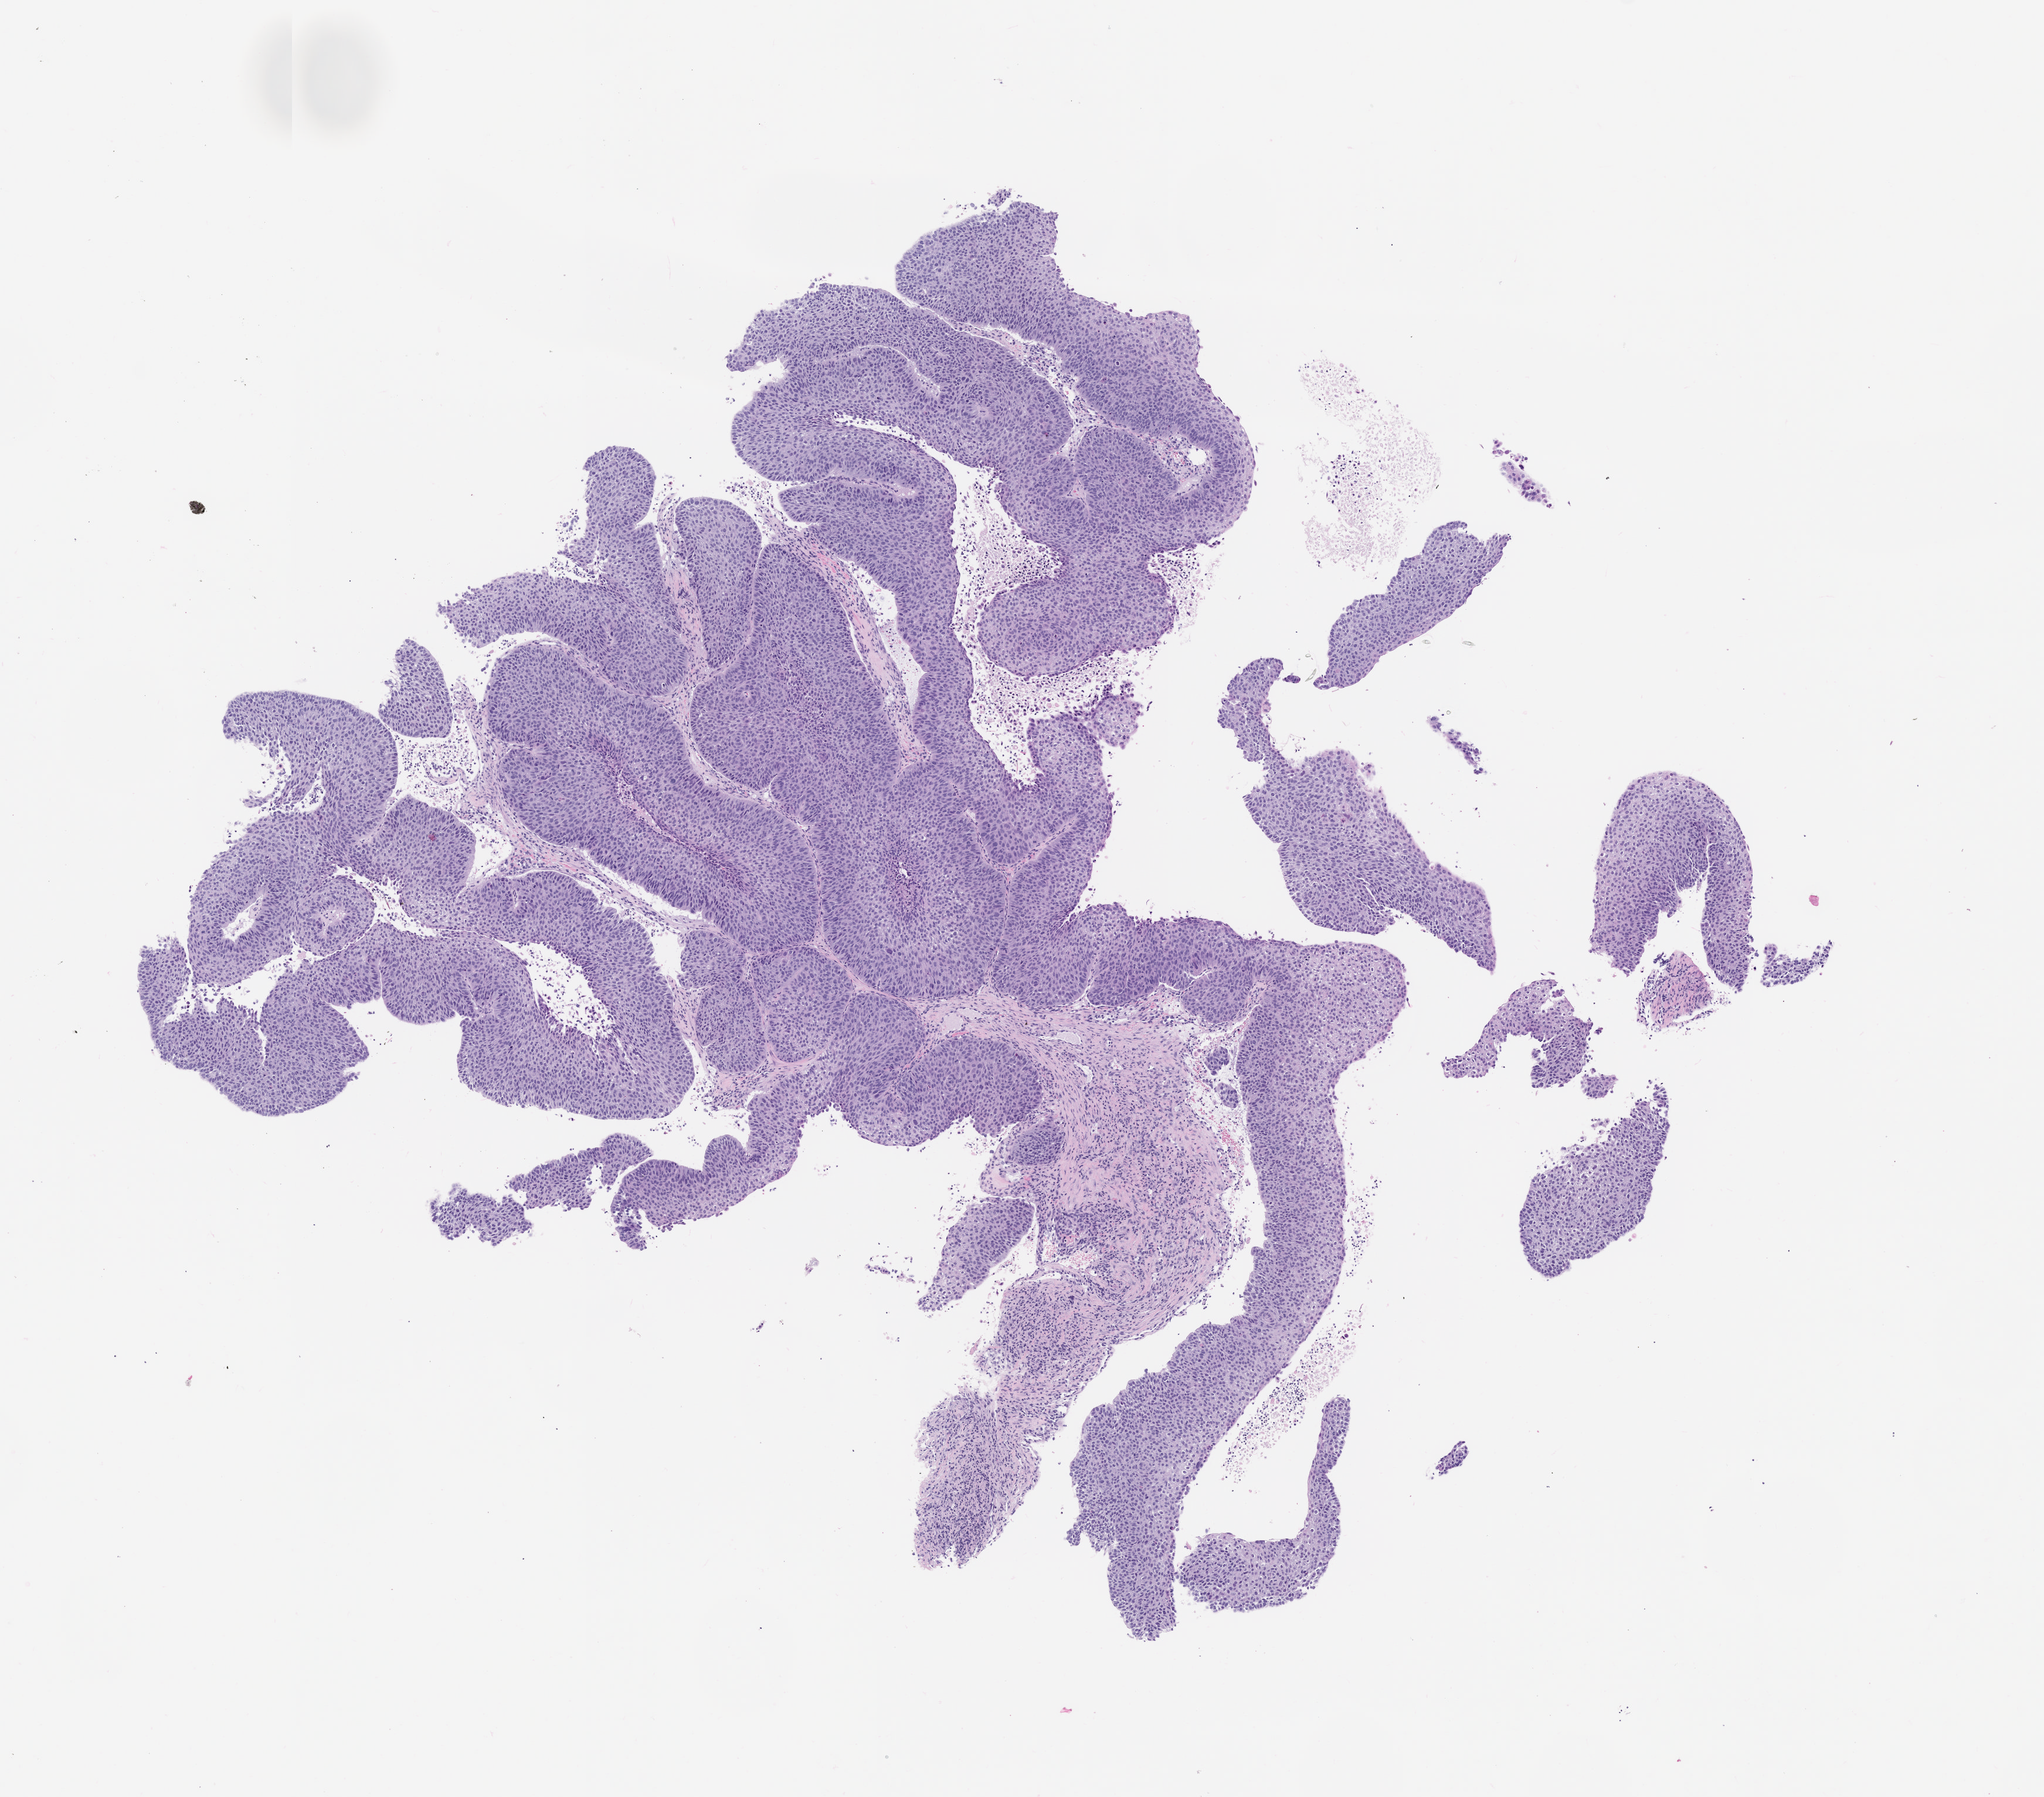
Haematoxylin and eosin whole-slide image of a patient-derived xenograft (PDX) tumor grown in a mouse, passage 3, shown as a low-resolution overview of the whole scanned area (about 7.0 x 6.2 mm). Formalin-fixed, paraffin-embedded (FFPE) tissue. Tumor site category: lung.
• originating patient diagnosis: Lung Squamous Cell Carcinoma